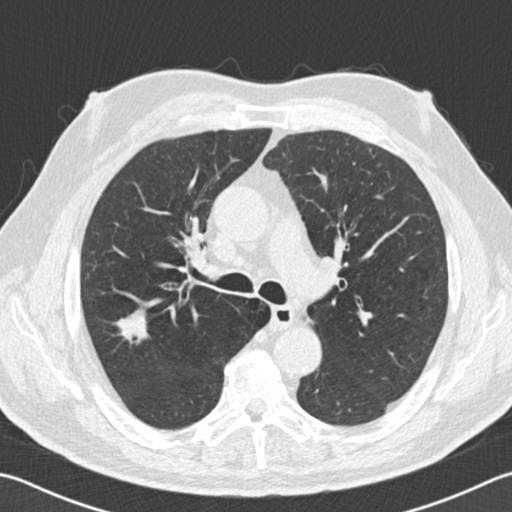
Low-dose screening chest CT, one axial slice; slice 108 of 162 in the series (ordered by position); 120 kVp; lung window (W 1500 / L -600 HU); 2 mm slice thickness; 512 × 512 image matrix, field of view 346 × 346 mm.
Structures marked on this image (outlined manually by an expert reader):
- lesion 1 (tumor, upper lobe of right lung): bounding box [x1, y1, x2, y2] px = [116, 310, 148, 343]